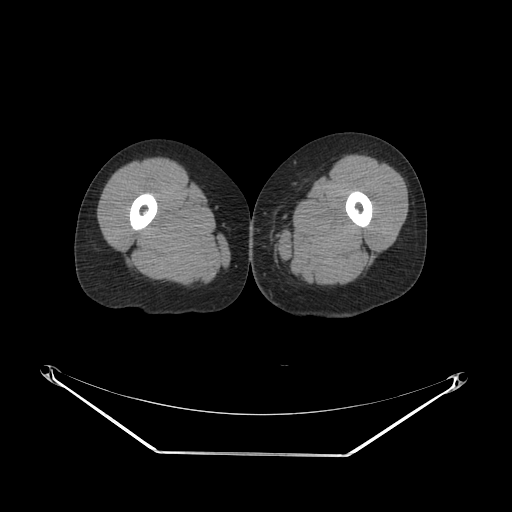
CT of an extremity soft-tissue mass (from a PET/CT study), one axial slice; position 31 of 267 along the scan axis; reconstruction kernel SOFT; 140 kVp; soft-tissue window (W 400 / L 40 HU); 3.75 mm slice thickness; 512 × 512 image matrix, field of view 500 × 500 mm. Female patient. From the clinical record (not read from this slice): histological type: leiomyosarcoma; grade: high; site of the primary tumour: groin.
Outlined on this slice (expert contour drawn on MRI and transferred to this co-registered scan by the dataset authors):
- gross tumour volume including surrounding oedema: box from (x=251, y=242) to (x=254, y=245) px